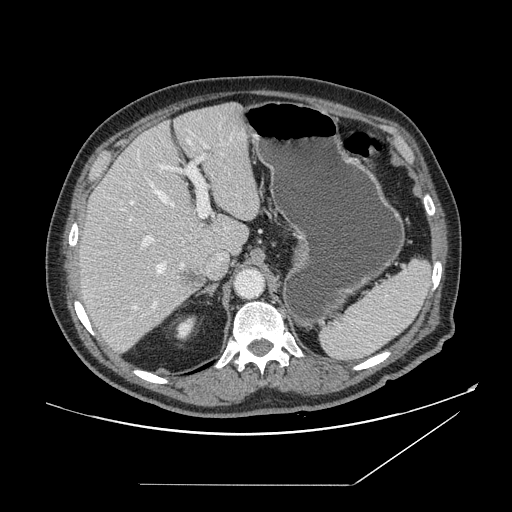
Contrast-enhanced abdominal CT, one axial slice; position 106 of 166 along the scan axis; 120 kVp; intravenous contrast given; soft-tissue window (W 400 / L 40 HU); 2.5 mm slice thickness; 512 × 512 image matrix, field of view 416 × 416 mm. Male patient, age 80 years. Case-level facts recorded for this patient, not image findings: diagnosis: colorectal cancer liver metastases, imaged before liver resection; multiple liver metastases: no; largest metastasis: 2.2 cm; disease in both lobes: no.
Outlined on this slice (manually delineated by an expert):
- hepatic veins: bounding box [x1, y1, x2, y2] px = [130, 139, 191, 310]
- liver: [79, 104, 260, 354]
- planned liver remnant (the part of the liver to remain after resection): [87, 104, 260, 258]
- portal vein (with intrahepatic branches): [124, 143, 210, 307]
- liver metastasis: [184, 272, 204, 291]
- liver metastasis: [180, 269, 204, 287]